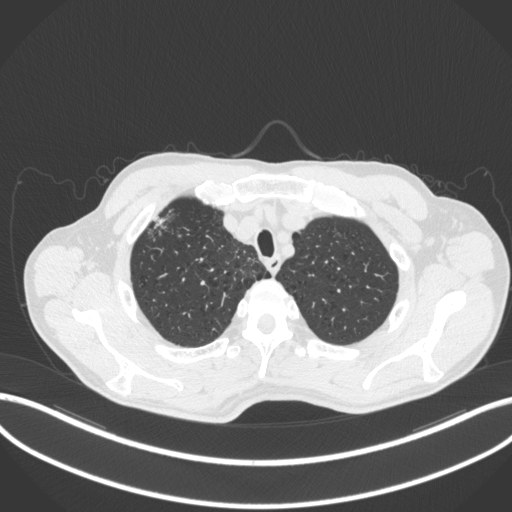
Chest CT, one axial slice; slice 364 of 414 in the series (ordered by position); reconstruction kernel B31f; lung window (W 1500 / L -600 HU); 512 × 512 image matrix. Male patient, age 69 years. From the clinical record (not read from this slice): clinical TNM (as recorded): T1b N1 M0.
Outlined on this slice (rectangle marked by the reading radiologist):
- lung tumour (recorded histology: adenocarcinoma): bounding box <148,206,176,238> (left, top, right, bottom; pixels)